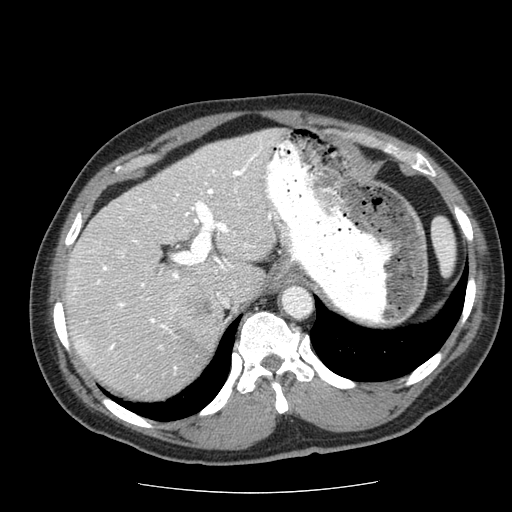
Contrast-enhanced abdominal CT (liver protocol), one axial slice. Soft-tissue window (W 400 / L 40 HU). 512 × 512 image matrix. From the clinical record (not read from this slice): diagnosis: hepatocellular carcinoma (patient treated with transarterial chemoembolisation; whether this scan precedes or follows treatment is not stated here); TNM stage (as recorded): Stage-IIIA; Child-Pugh class: A; tumour nodularity: multinodular; tumour size: 8 cm.
Outlined on this slice (semi-automatic segmentation, software-assisted and operator-edited):
- liver parenchyma outside the tumour (the mass and vessels are separate outlines, so this box may not span the whole liver): bounding box [x1, y1, x2, y2] px = [64, 128, 280, 398]
- mass: [173, 290, 220, 365]
- liver vessels: [72, 146, 271, 377]